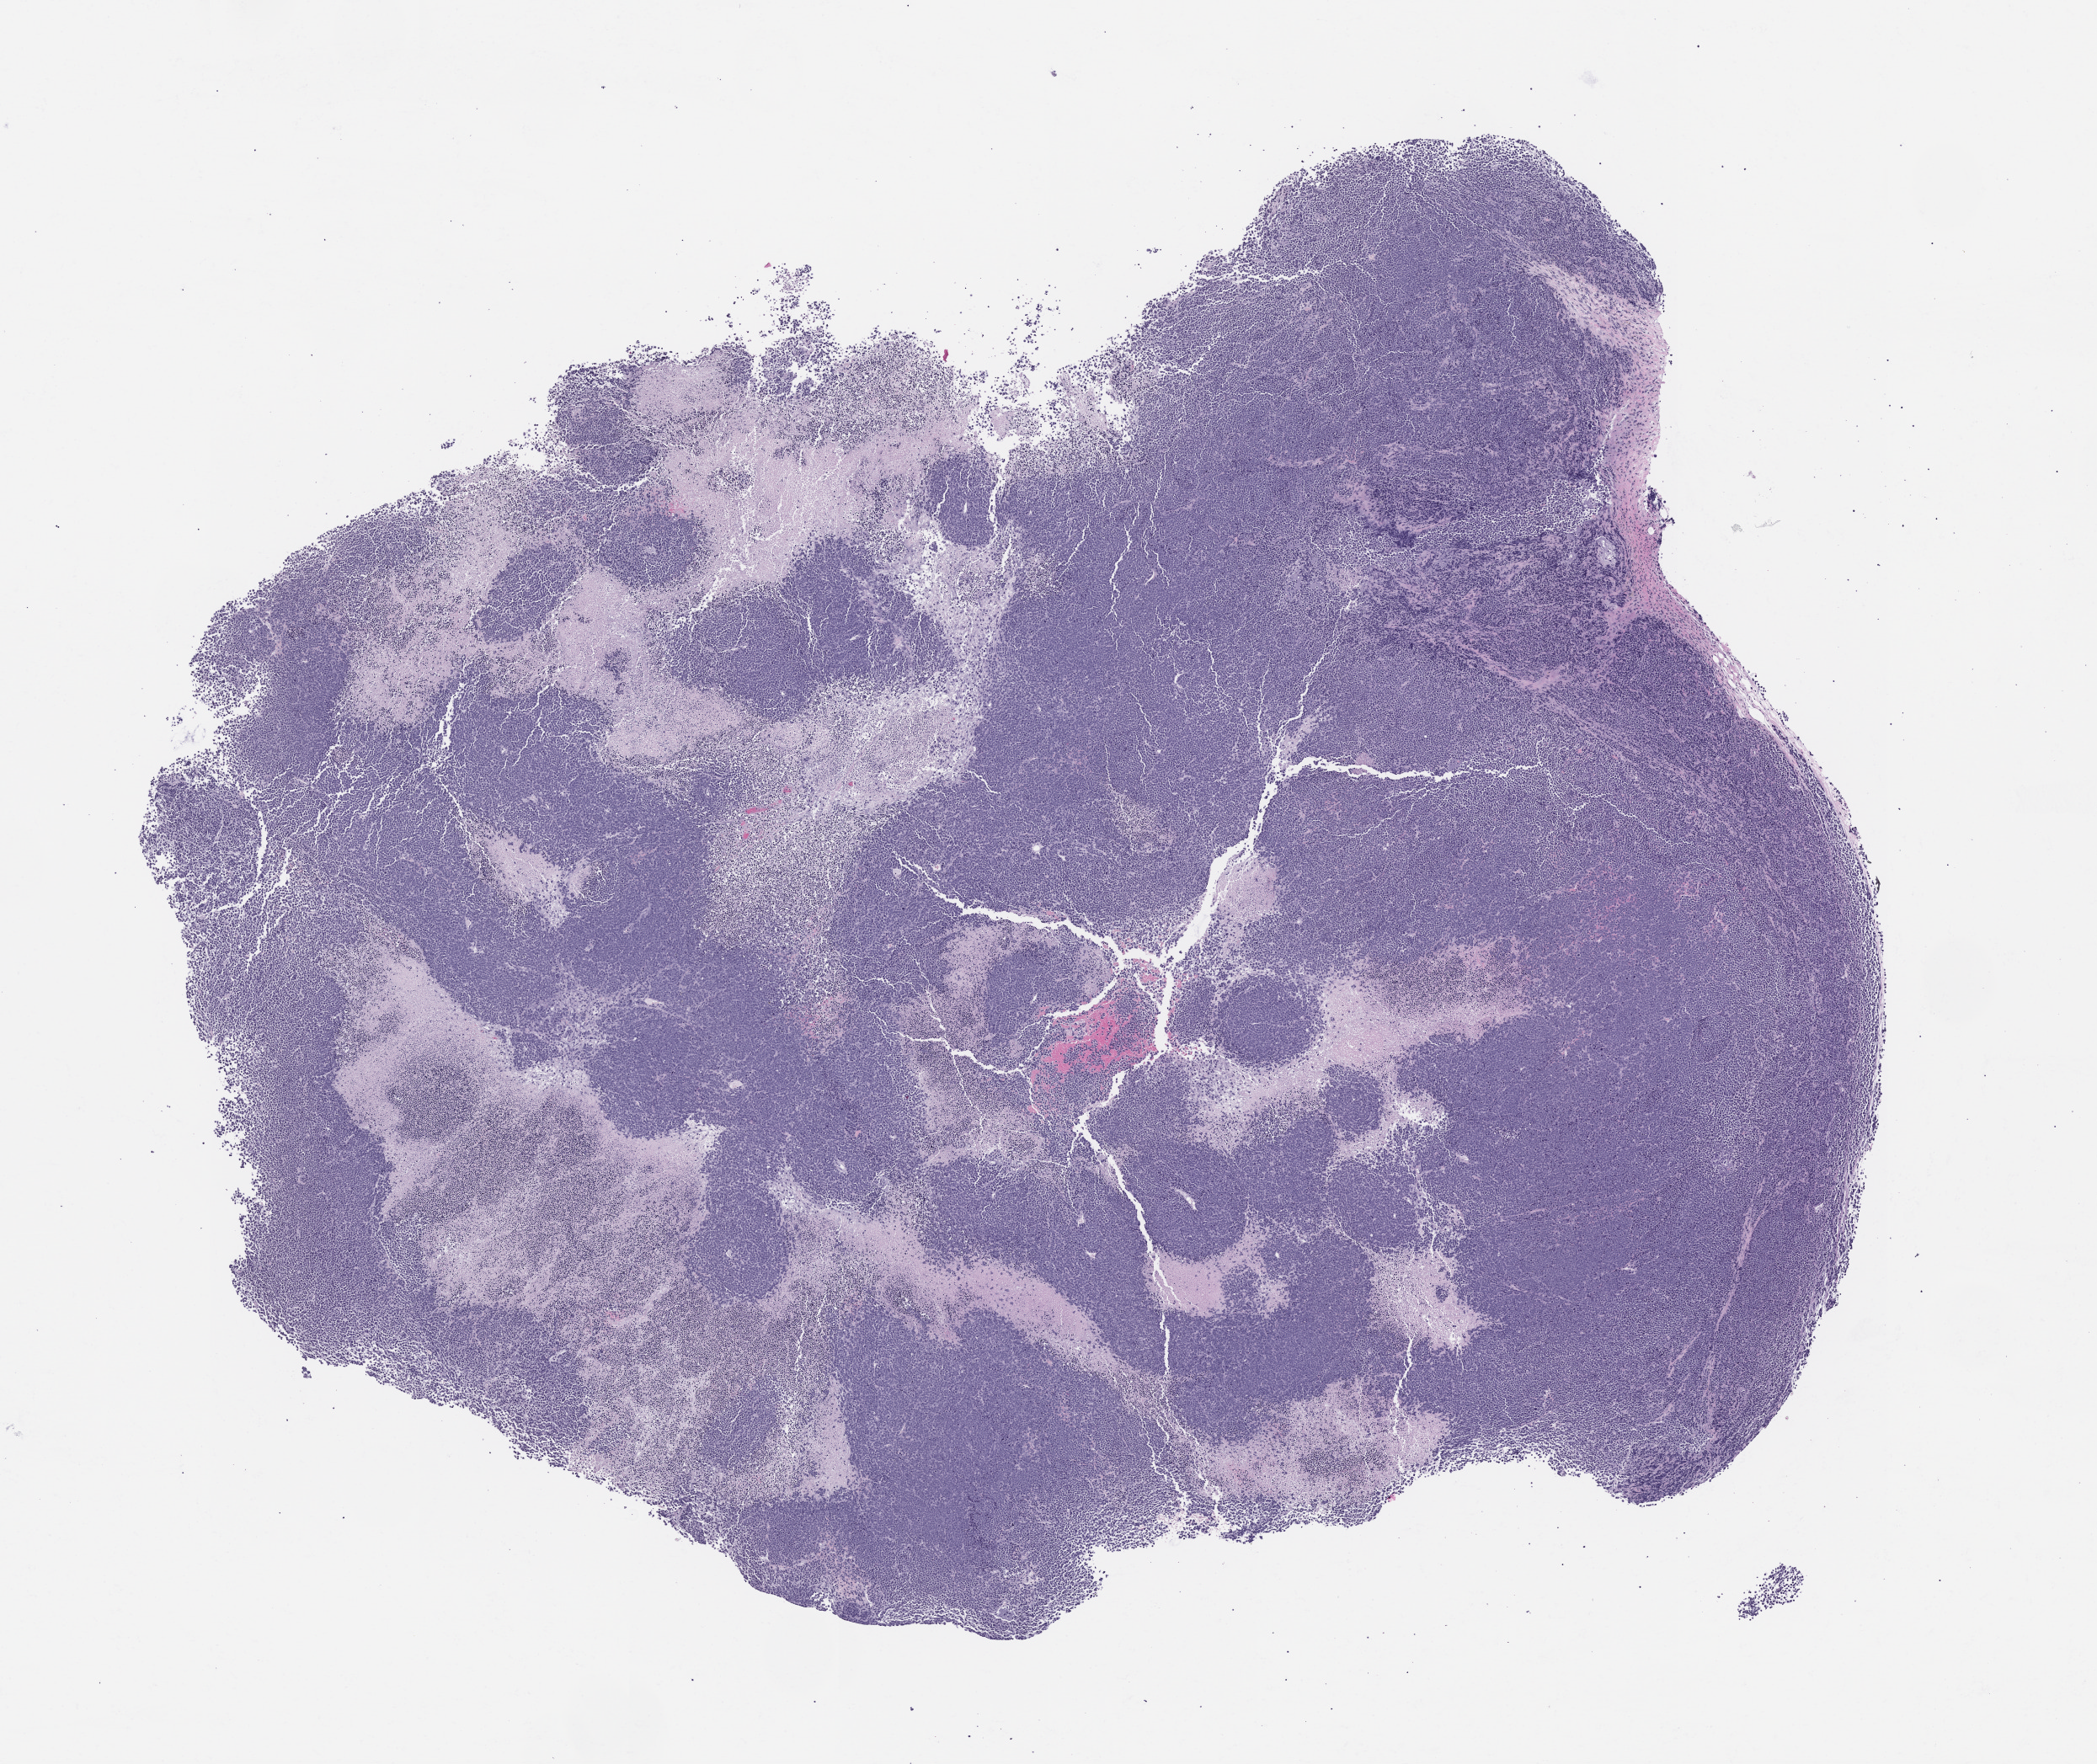
Haematoxylin and eosin whole-slide image of a patient-derived xenograft (PDX) tumor grown in a mouse, passage 1 — whole scanned area (about 10.0 x 8.4 mm) shown as a low-resolution overview, formalin-fixed paraffin-embedded section, tumor site category: endocrine.
Originating patient diagnosis: Merkel Cell Carcinoma.